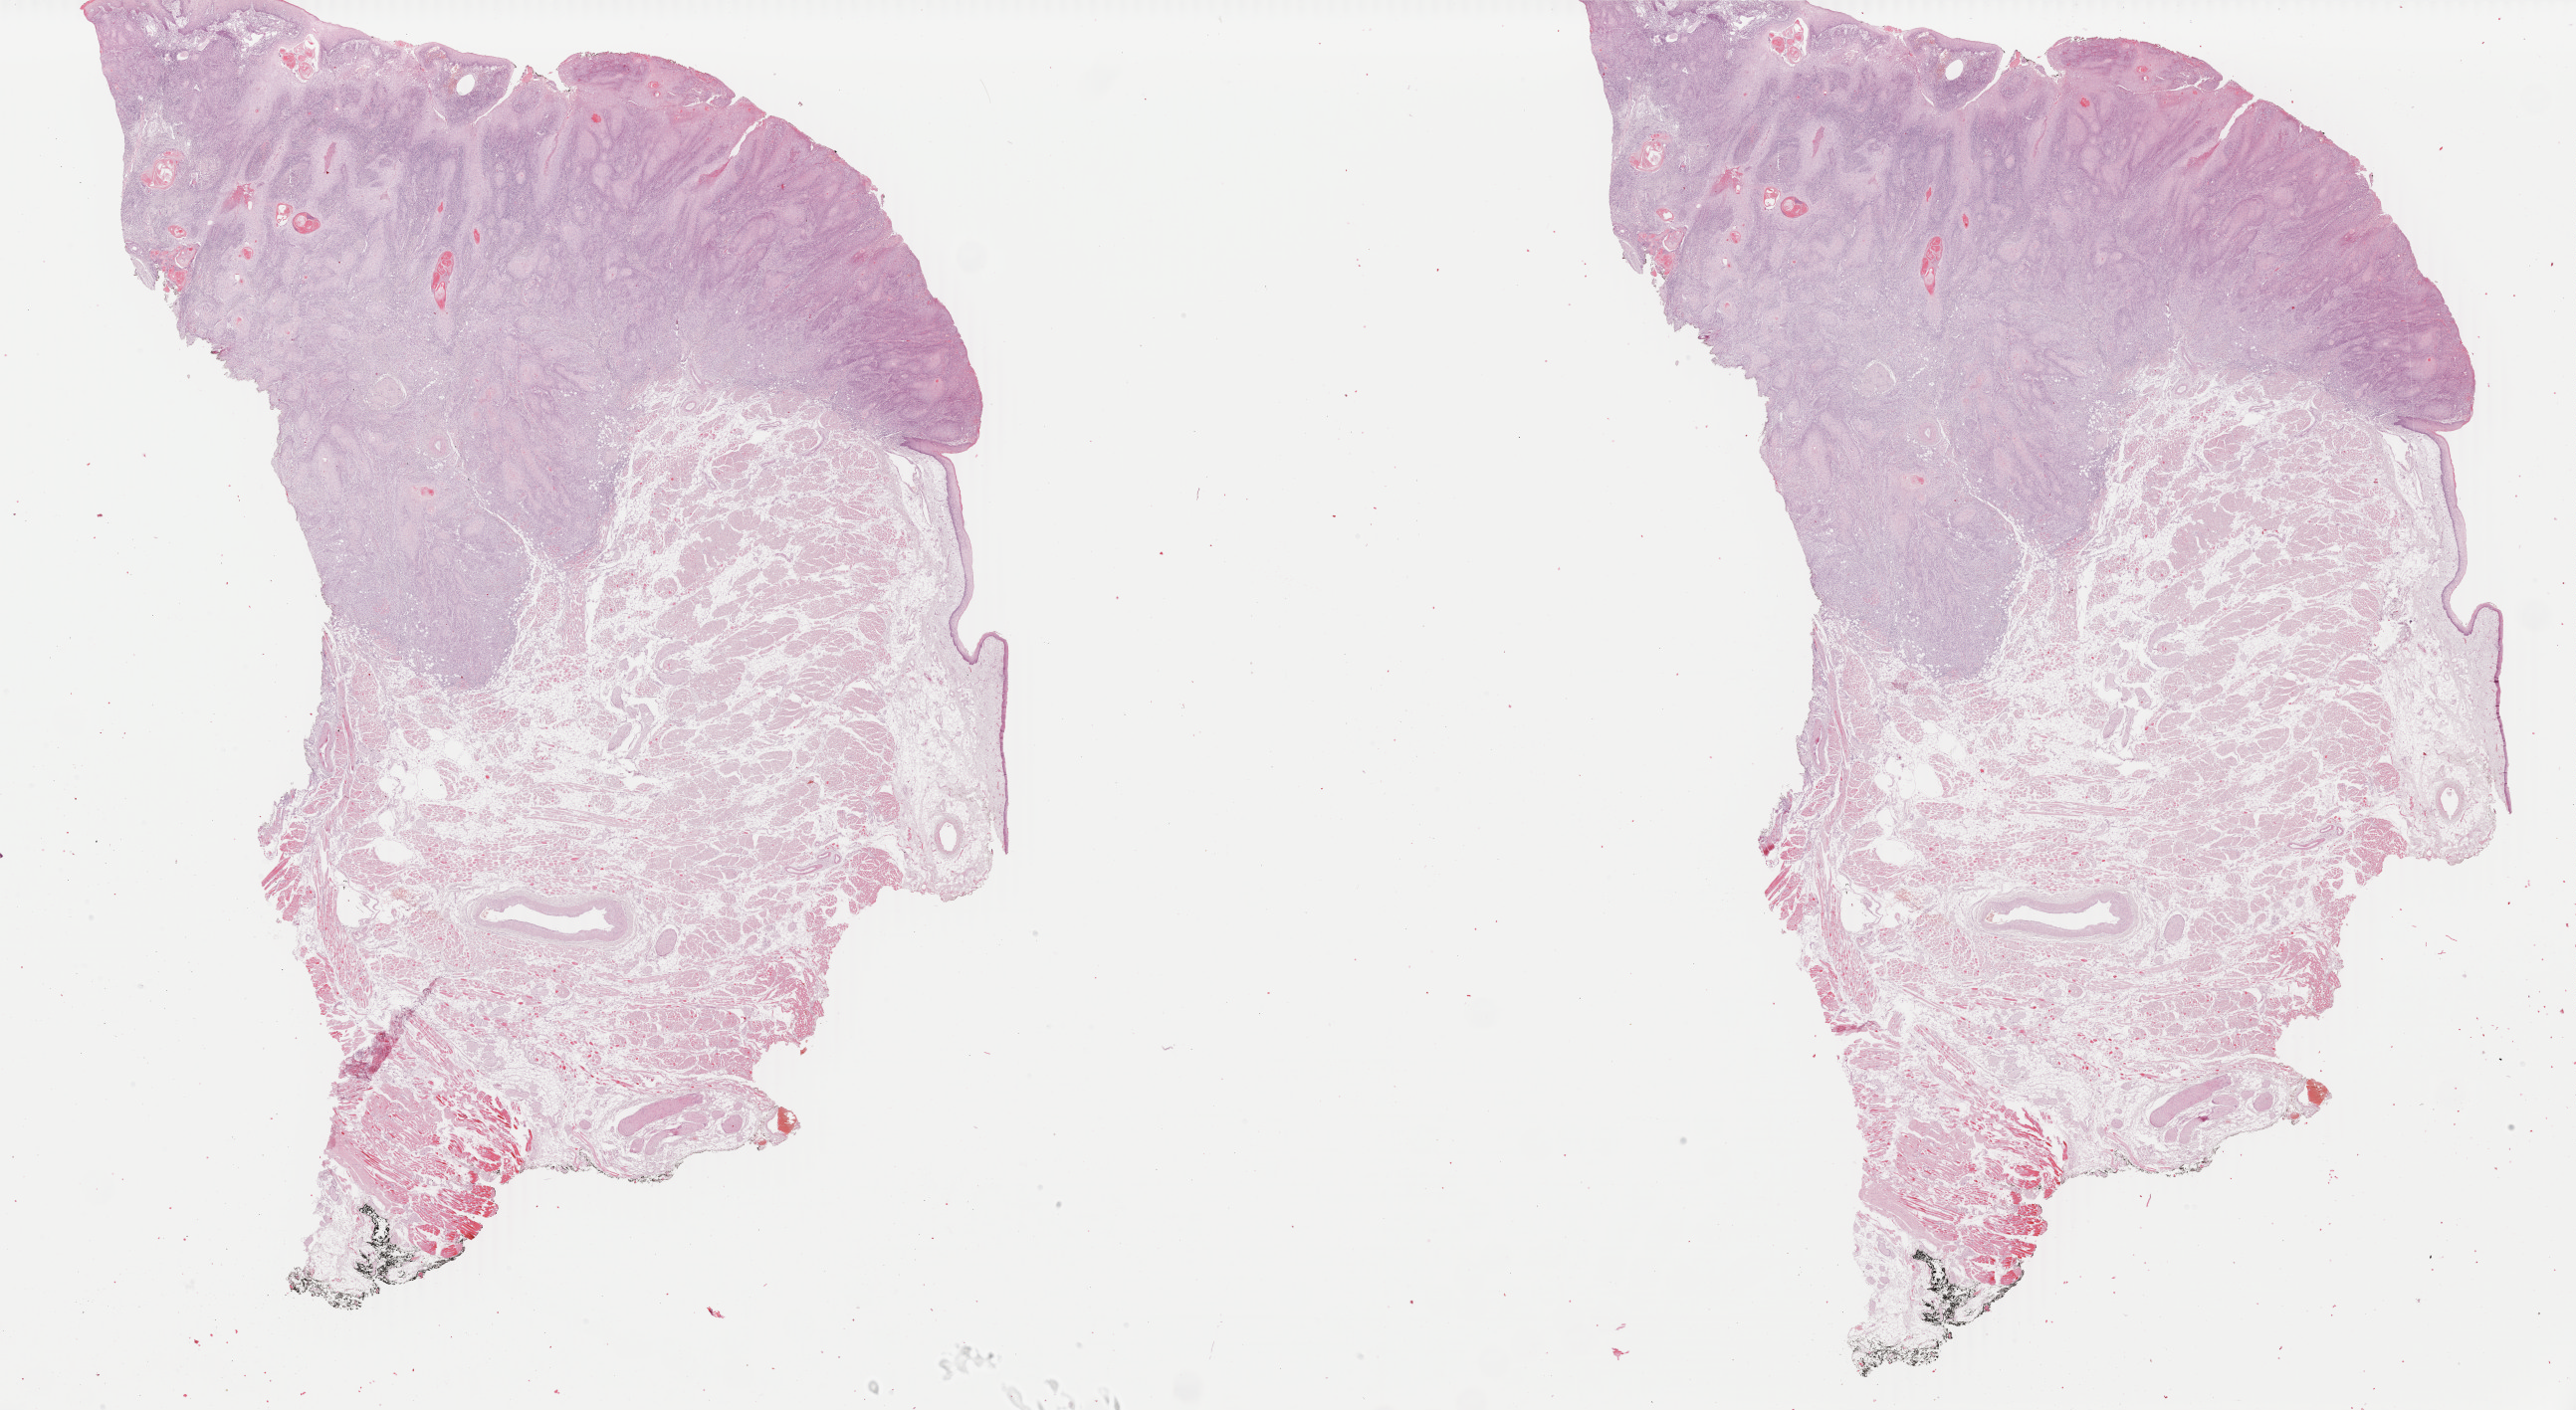
Whole-slide histology image, H&E — a low-resolution overview of the entire scanned area, about 41.2 x 22.5 mm (slide scanned at 40x), FFPE section, primary tumour sample from the head and neck. Male patient; age at initial diagnosis 73 years. Histologic grade: G2 (moderately differentiated).
TNM: T1 N0. Diagnosis: Squamous cell carcinoma, NOS (tongue, NOS). AJCC pathologic stage: I.